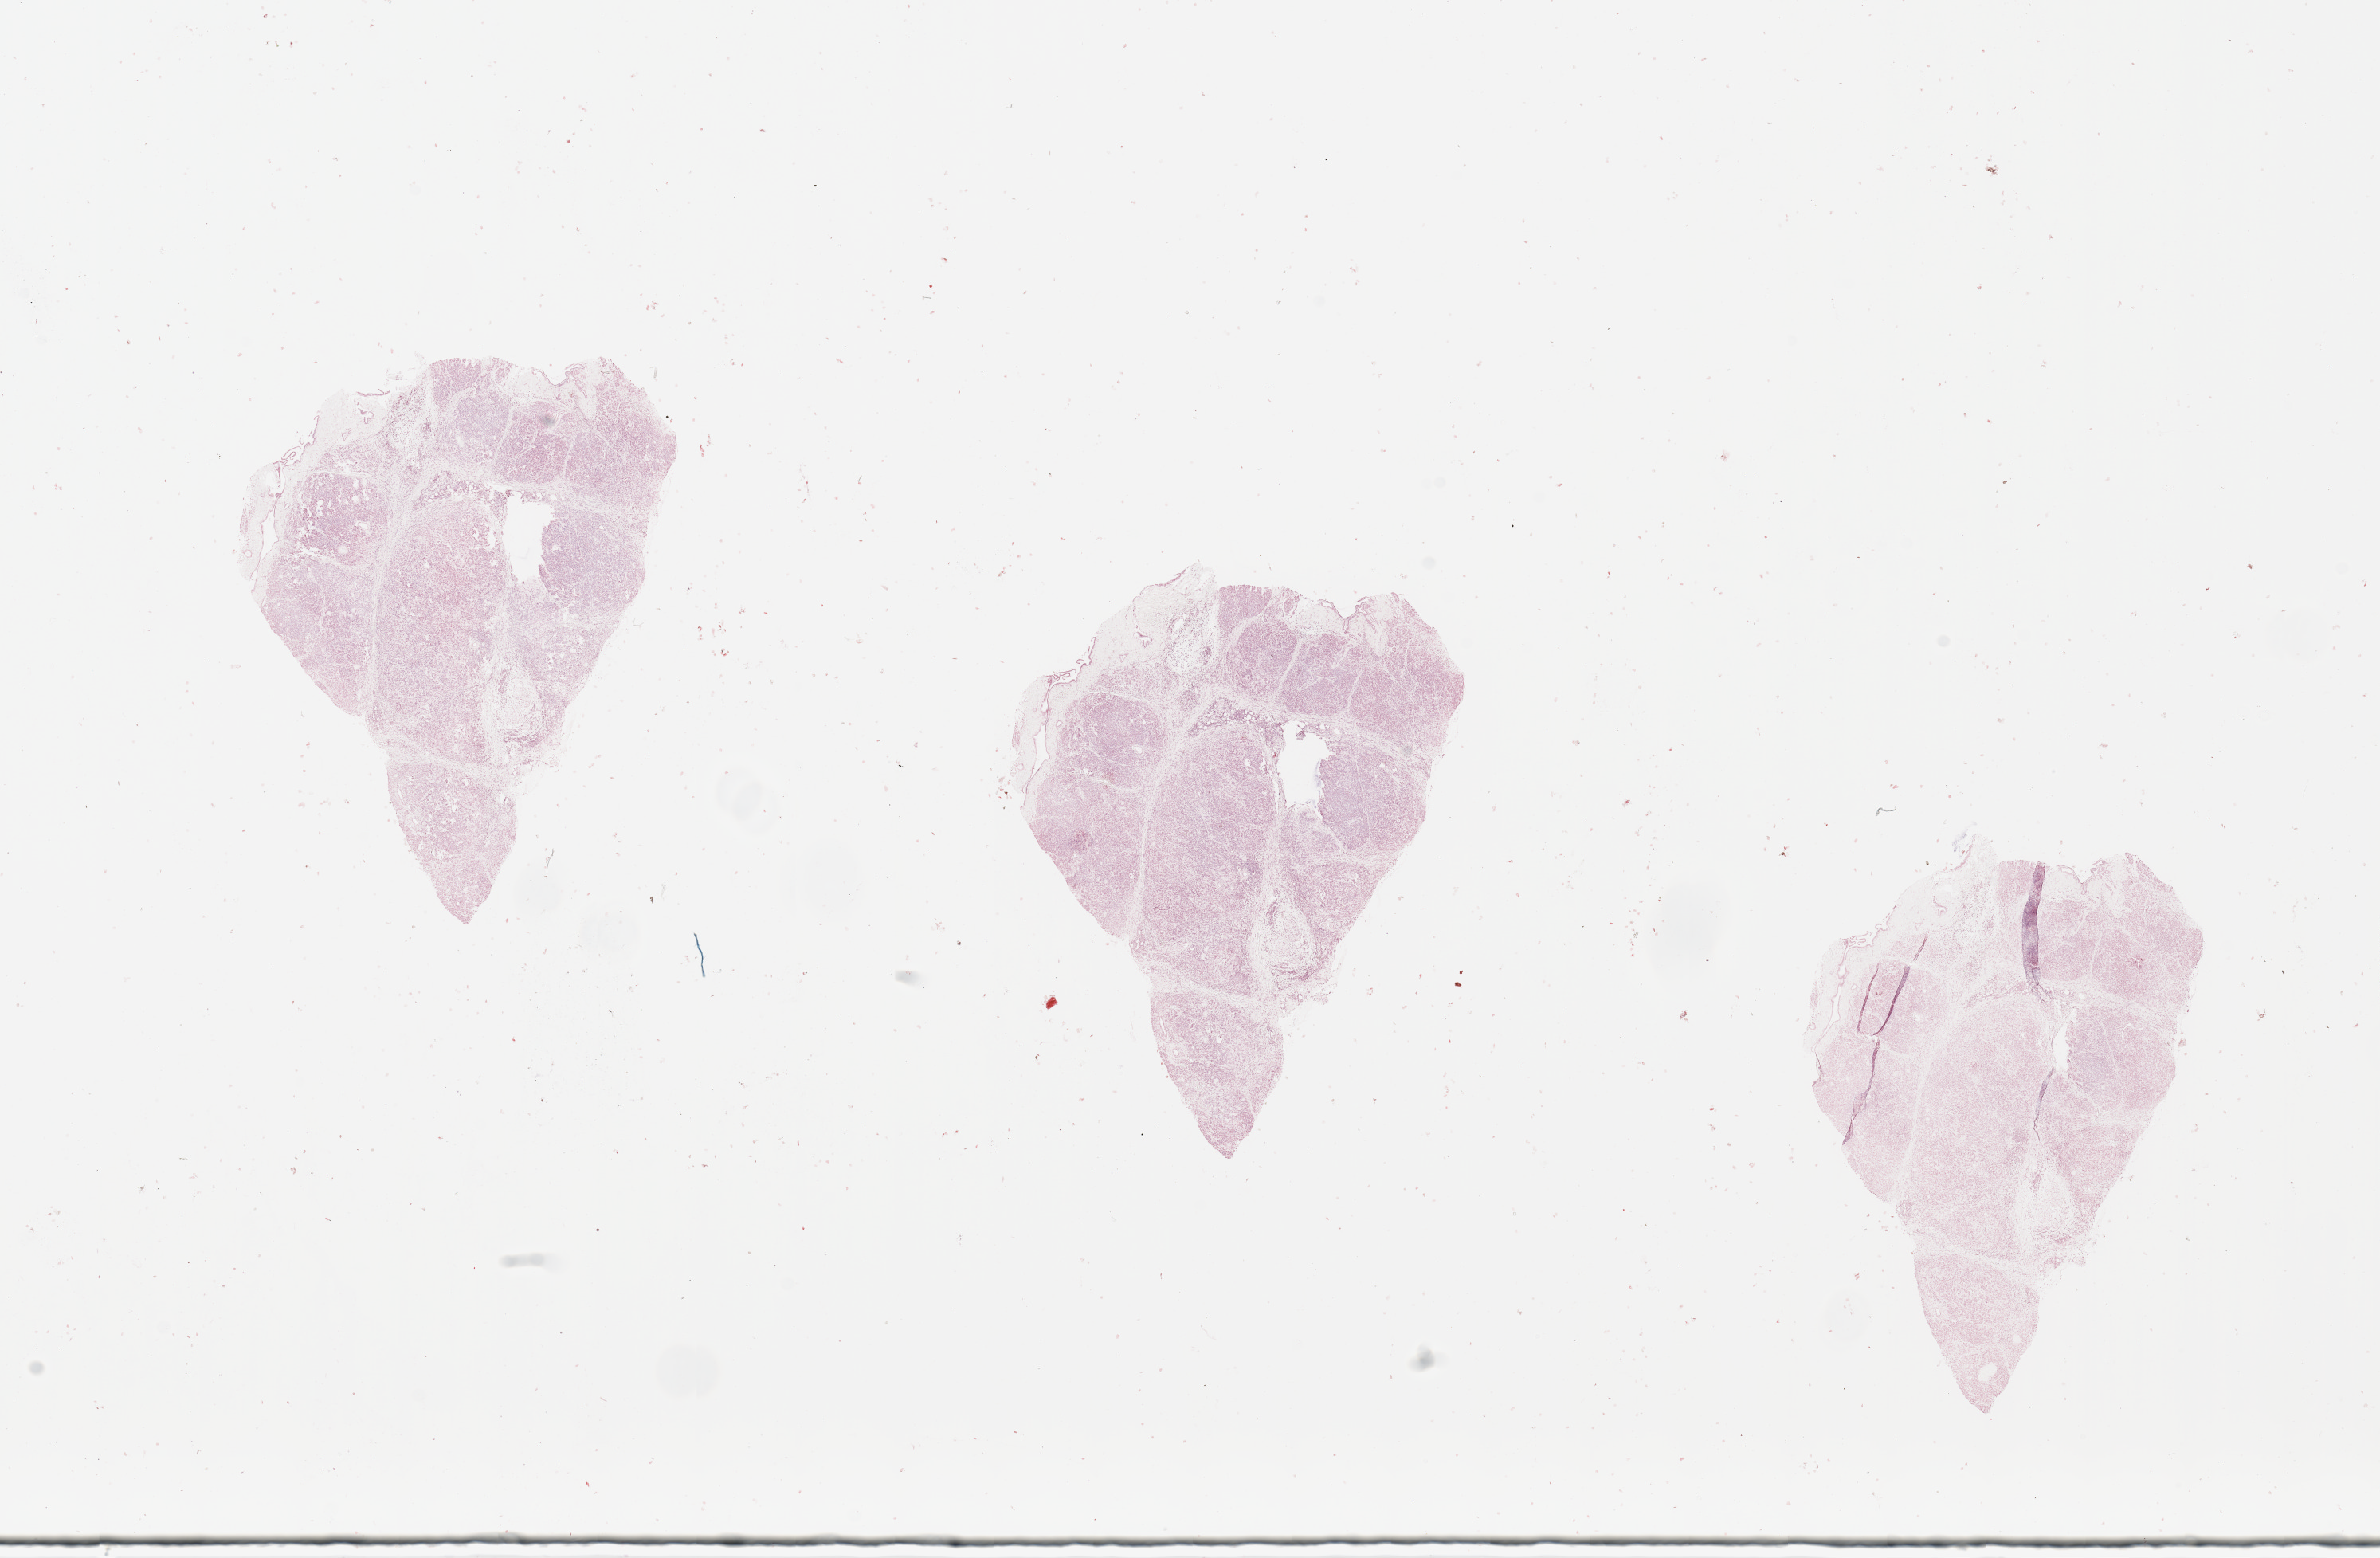
Hematoxylin and eosin (H&E) stained whole-slide image — low-resolution overview of the scanned area, about 23.6 x 15.5 mm (slide scanned at 20x). Normal (non-tumour) tissue sample, sampled site: pancreas. 71-year-old male patient.
This section: normal (non-tumour) tissue from the same patient. Patient diagnosis: Infiltrating duct carcinoma, NOS.